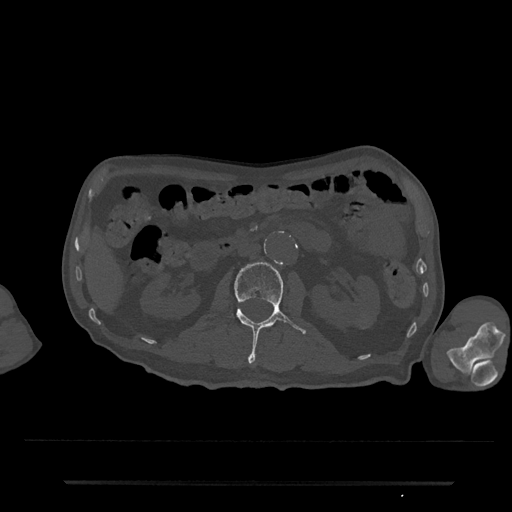
CT including the spine, one axial slice; position 60 of 797 along the scan axis; reconstruction kernel Br40s/3; 120 kVp; bone window (W 1800 / L 400 HU); 512 × 512 image matrix. Male patient, age 74 years. From the clinical record (not read from this slice): primary cancer: prostate.
Annotated regions visible in this slice (semi-automatically segmented with operator editing):
- L2 vertebra: bounding box (x1, y1, x2, y2) in pixels: (229, 262, 307, 363)